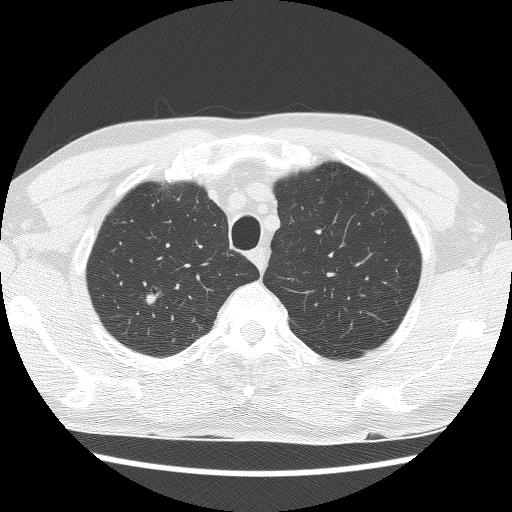
Low-dose screening chest CT, one axial slice. Slice 129 of 157 in the series (ordered by position). 120 kVp. Lung window (W 1500 / L -600 HU). 2.5 mm slice thickness. 512 × 512 image matrix, field of view 340 × 340 mm.
Annotated regions visible in this slice (expert manual segmentation):
- lesion 1 (tumor, upper lobe of right lung): box from (x=145, y=291) to (x=163, y=306) px